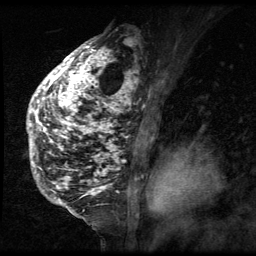
Breast MRI (dynamic contrast-enhanced), one sagittal slice. Slice 39 of 64 in the series (ordered by position). 3 images stored at this slice position (order not interpretable as contrast timing). 1.5 T. TE 4.2 ms, TR 9 ms. 2.5 mm slice thickness. 256 × 256 image matrix, field of view 180 × 180 mm. Patient: female, 50 years. Case-level facts recorded for this patient, not image findings: setting: breast cancer imaged before/during neoadjuvant chemotherapy; receptor status: triple-negative.
Outlined on this slice (semi-automatic segmentation, software-assisted and operator-edited):
- analysis volume of interest (the breast-tissue region the enhancement analysis was run in; not a lesion): box from (x=27, y=39) to (x=140, y=212) px
- tumour enhancement mask (voxels above the 140 % enhancement threshold inside the analysis volume of interest): (x=27, y=39)–(x=140, y=212)